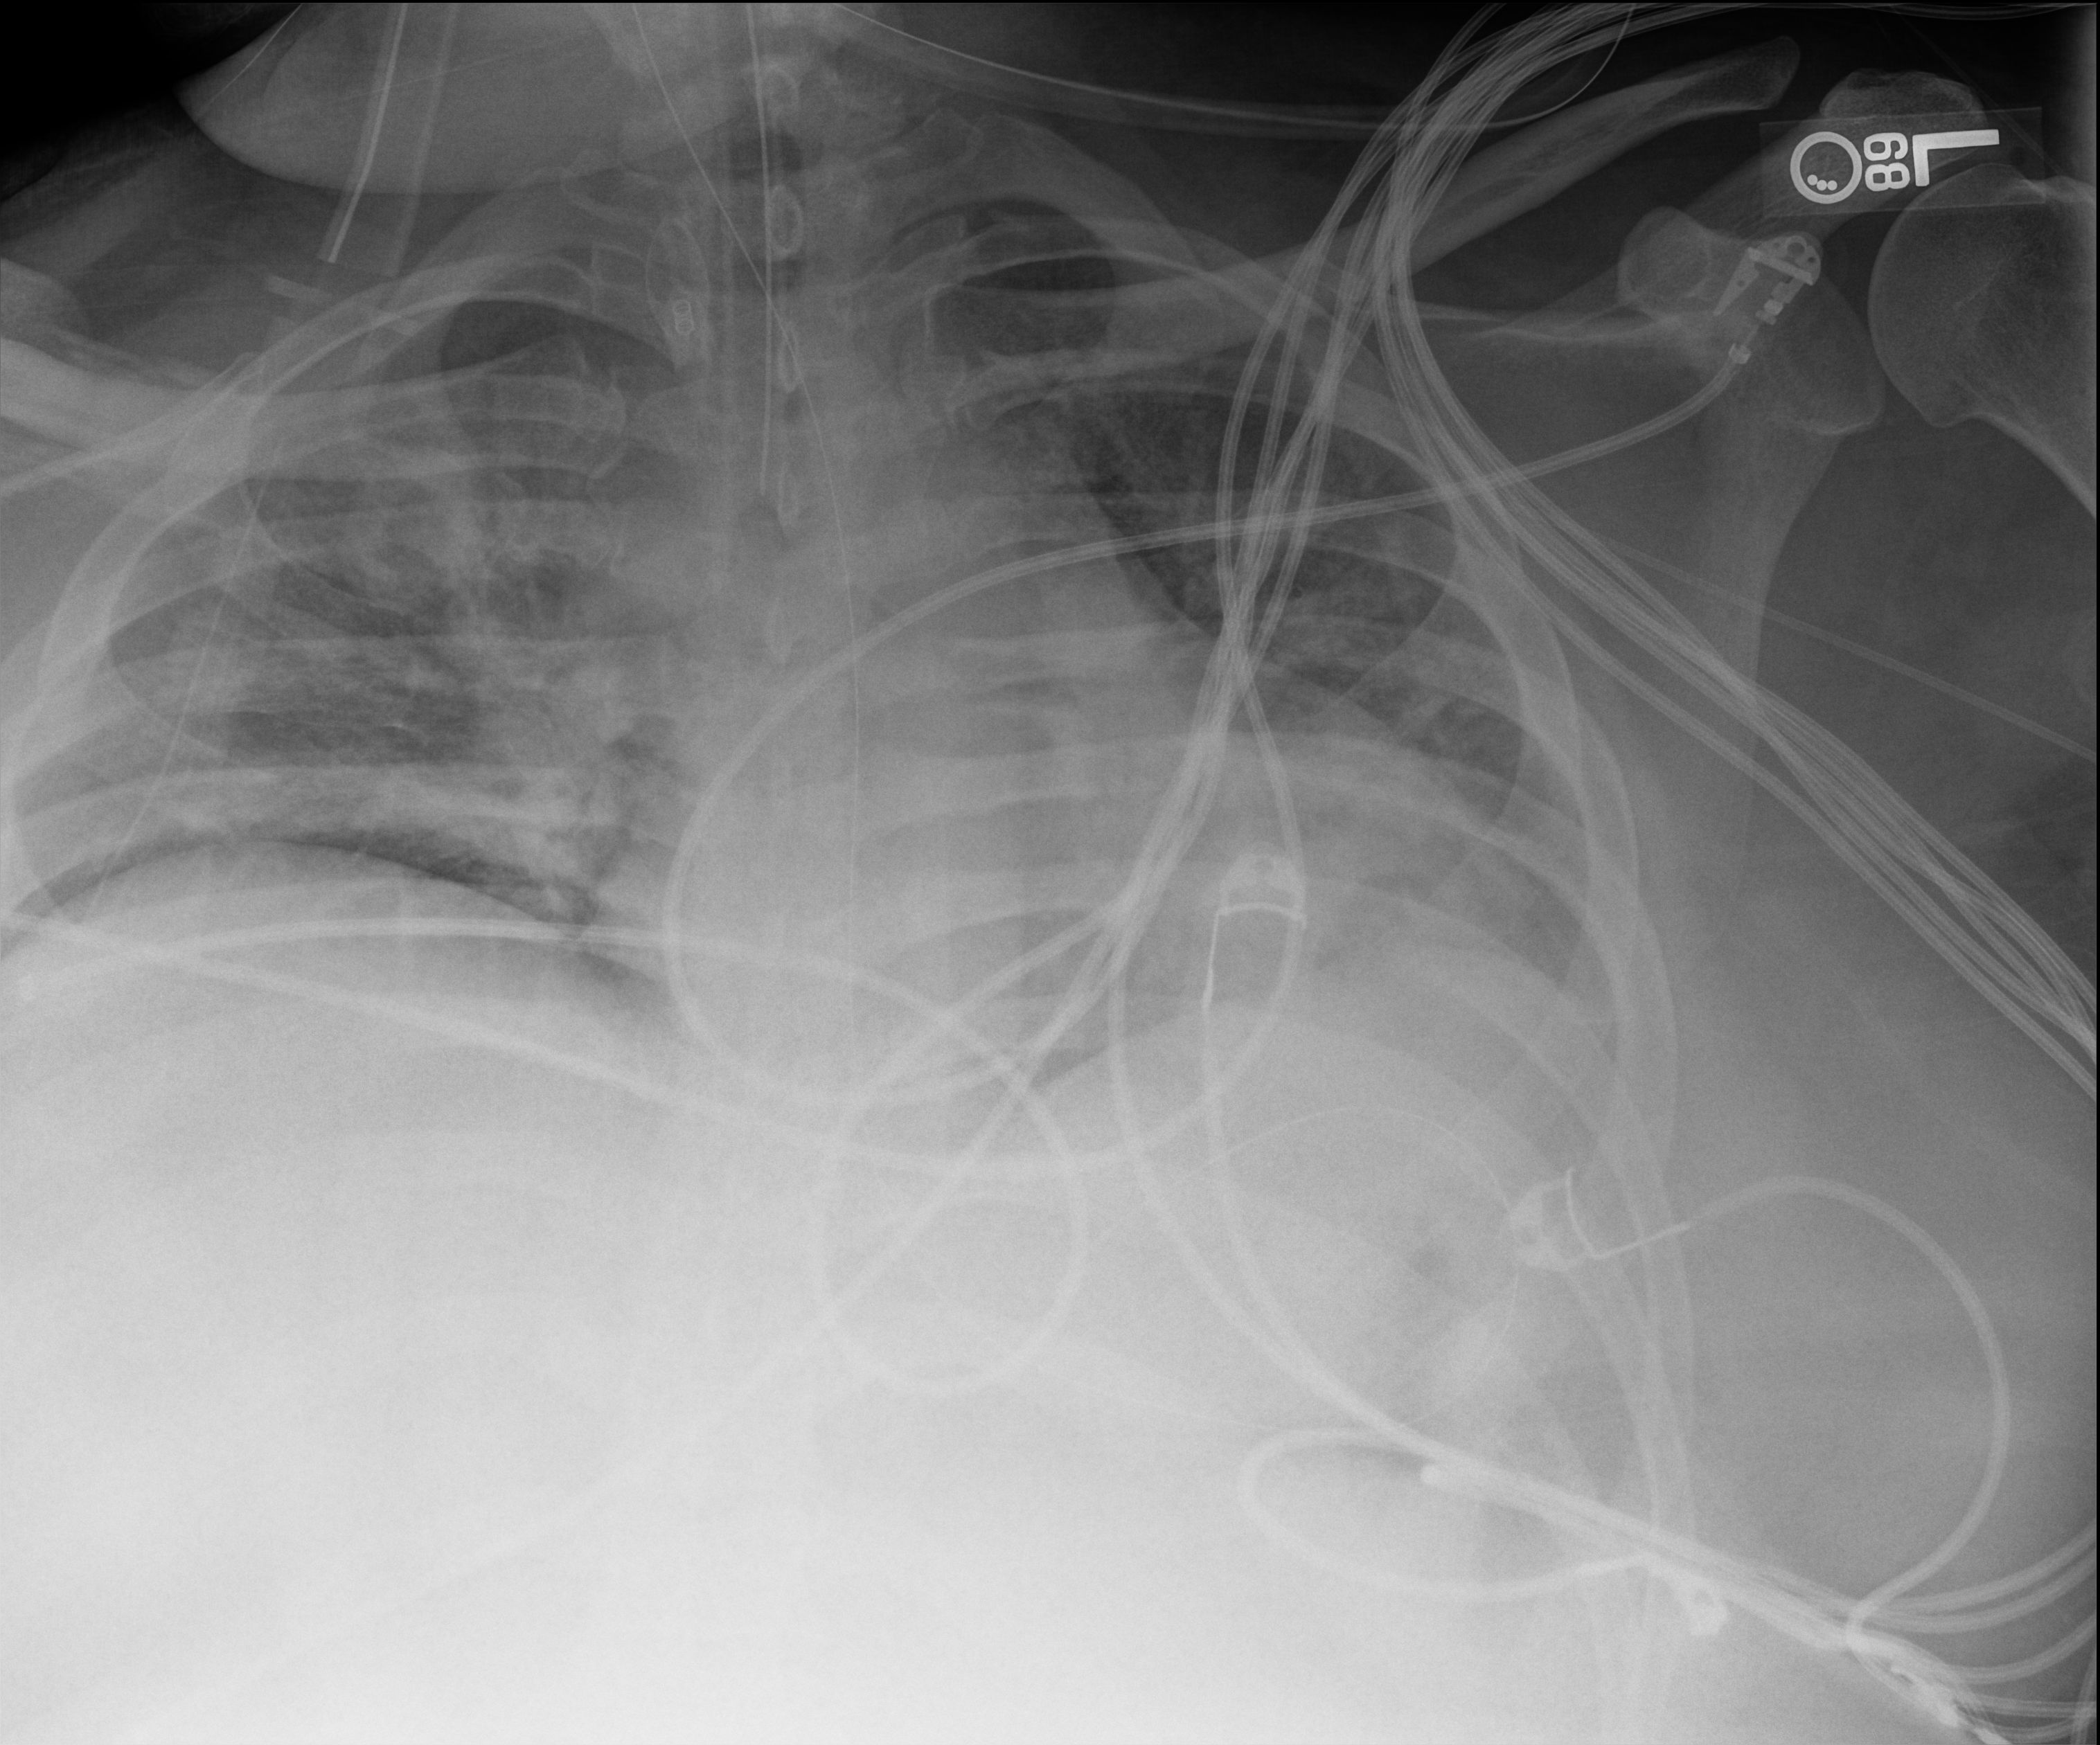
Bedside chest radiograph (digital radiography), anteroposterior (AP) projection. Patient hospitalised with COVID-19; male, aged 18–59 years.
Hospital-stay facts (about this admission, not read from this image; timing relative to this image not recorded): admitted to intensive care during this hospital stay: yes.